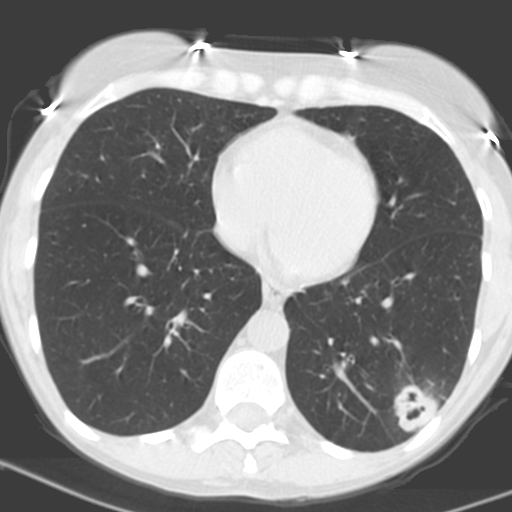
Axial slice from a low-dose chest CT screening exam; baseline annual screen; lung window (W 1500 / L -600 HU); 3.2 mm slice thickness; 512 × 512 image matrix. Female participant, aged 56 years at enrolment.
- Expert reader's lesion annotation, bounding box (x1, y1, x2, y2) in pixels: (372, 366, 454, 439).
- Screening reader's record for this exam (one nodule recorded; not confirmed to be the boxed lesion): non-calcified nodule or mass ≥4 mm, left lower lobe, 31 × 23 mm, poorly defined margins, soft tissue attenuation, pre-existing on the prior screen: no.
- Official screen result: positive, change unspecified: nodule(s) >= 4 mm or enlarging nodule(s), mass(es), or other non-specific abnormalities suspicious for lung cancer.
- Lung cancer was diagnosed 27 days after this screen: squamous cell carcinoma, NOS, left lower lobe, poorly differentiated (G3), stage IB (AJCC 6th edition), 35 mm at pathology.